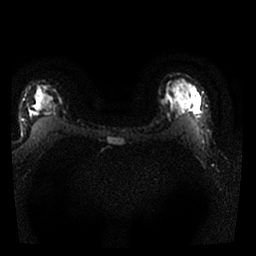
Breast MRI, one axial slice; slice 19 of 25 in the series (ordered by position); diffusion-weighted series; image 2 of 4 stored at this slice position (different b-values; order by instance number); 1.5 T; 4 mm slice thickness; 256 × 256 image matrix, field of view 300 × 300 mm. Female patient.
Outlined on this slice (manually delineated by an expert):
- tumour on diffusion-weighted imaging: bounding box [x1, y1, x2, y2] px = [161, 91, 175, 112]